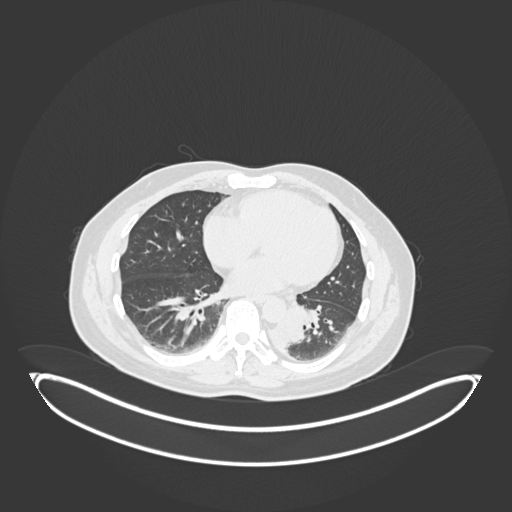
Chest CT, one axial slice. Reconstruction kernel B30f. 120 kVp. Lung window (W 1500 / L -600 HU). 1 mm slice thickness. 512 × 512 image matrix, field of view 500 × 500 mm. Male patient, age 54 years. Case-level facts recorded for this patient, not image findings: clinical TNM (as recorded): T3 N0 M0.
Structures marked on this image (rectangle marked by the reading radiologist):
- lung tumour (recorded histology: squamous cell carcinoma): bounding box (x1, y1, x2, y2) in pixels: (271, 312, 305, 354)